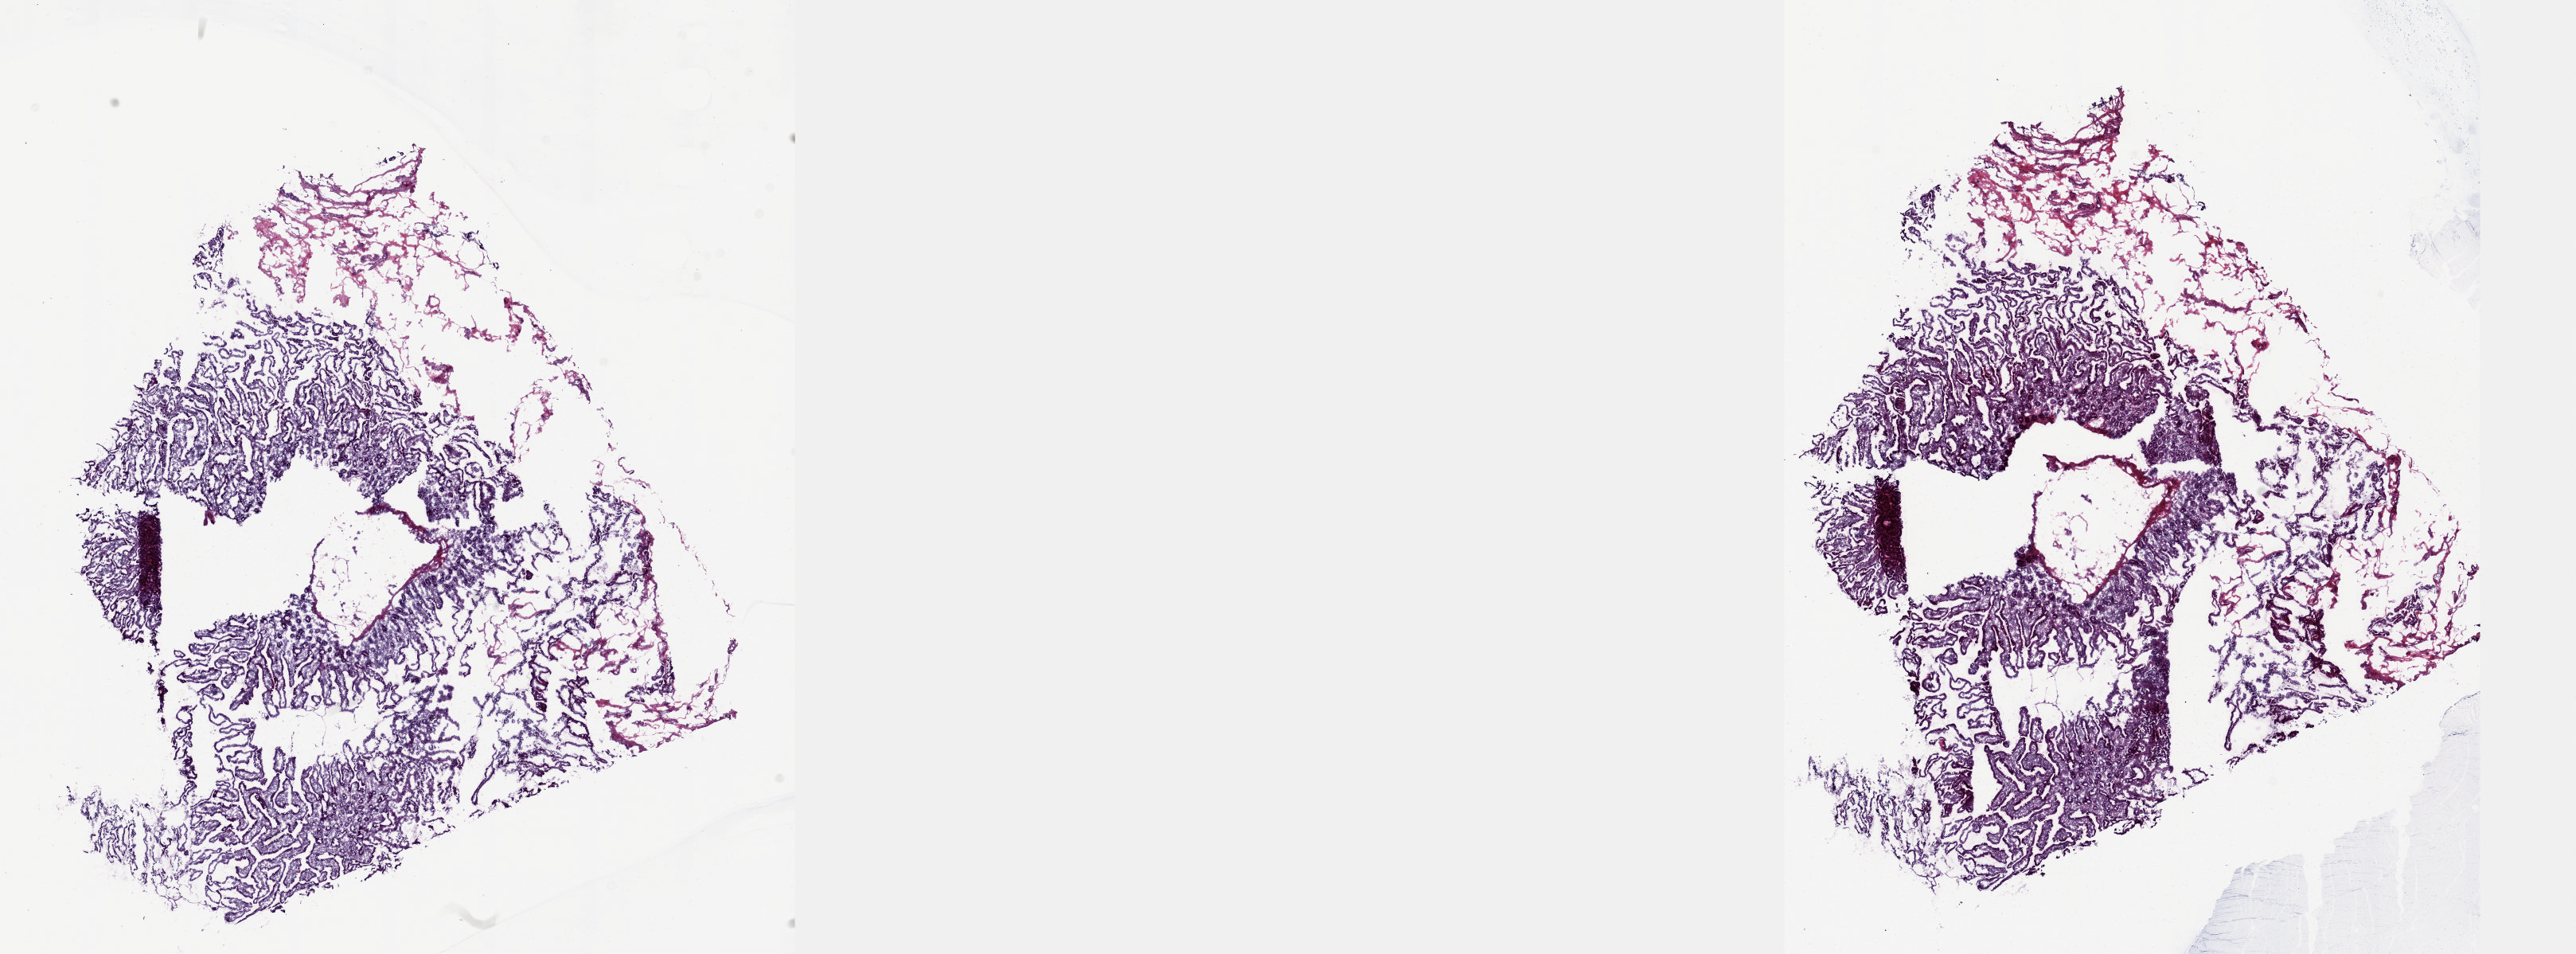
H&E whole-slide image — shown as a low-resolution overview of the whole scanned area (about 26.1 x 9.7 mm), frozen section from the top of the tissue portion, solid tissue normal (non-tumour tissue) sample from the pancreas. Female, age 65 years at initial diagnosis. Pathologist review of this section (percent, as recorded): tumour cells 0%, tumour nuclei 0%, normal cells 100%, stromal cells 0%, necrosis 0%. Inflammatory infiltration, as recorded: lymphocyte infiltration 3%, monocyte infiltration 0%, neutrophil infiltration 0%.
This section: solid tissue normal (non-tumour) sample from the same patient. Patient diagnosis: Infiltrating duct carcinoma, NOS.